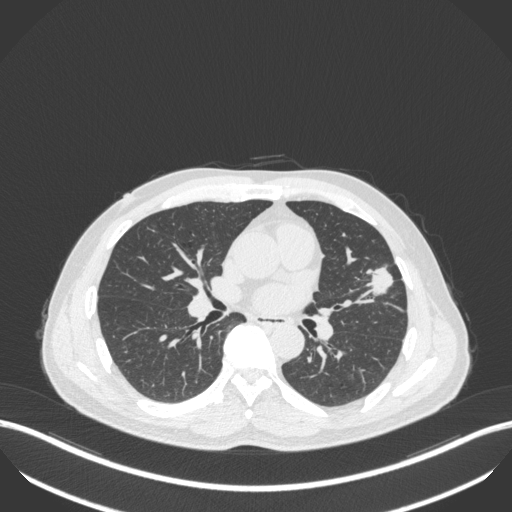
Chest CT, one axial slice; position 210 of 418 along the scan axis; 120 kVp; lung window (W 1500 / L -600 HU); 1 mm slice thickness; 512 × 512 image matrix, field of view 400 × 400 mm. Male patient, age 55 years. From the clinical record (not read from this slice): clinical TNM (as recorded): T1c N0 M0.
Outlined on this slice (rectangle marked by the reading radiologist):
- lung tumour (recorded histology: adenocarcinoma): bounding box (x1, y1, x2, y2) in pixels: (362, 261, 398, 302)